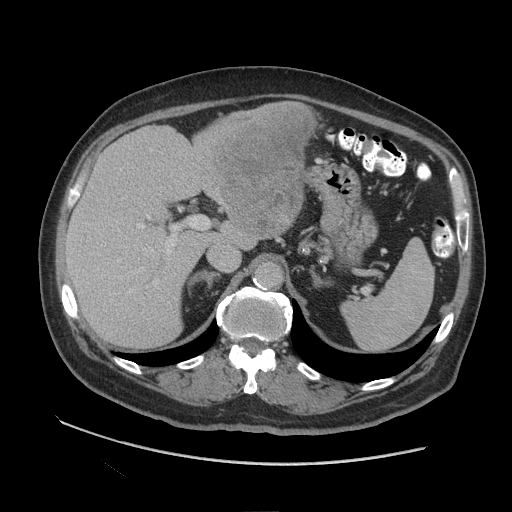
Contrast-enhanced abdominal CT (liver protocol), one axial slice; position 59 of 109 along the scan axis; reconstruction kernel STANDARD; 140 kVp; soft-tissue window (W 400 / L 40 HU); 2.5 mm slice thickness; 512 × 512 image matrix. From the clinical record (not read from this slice): diagnosis: hepatocellular carcinoma (patient treated with transarterial chemoembolisation; whether this scan precedes or follows treatment is not stated here); TNM stage (as recorded): Stage-I; Child-Pugh class: A; tumour nodularity: uninodular.
Structures marked on this image (semi-automatically segmented with operator editing):
- liver parenchyma outside the tumour (the mass and vessels are separate outlines, so this box may not span the whole liver): box from (x=66, y=108) to (x=316, y=348) px
- mass: (x=208, y=101)–(x=317, y=239)
- liver vessels: (x=67, y=215)–(x=177, y=293)